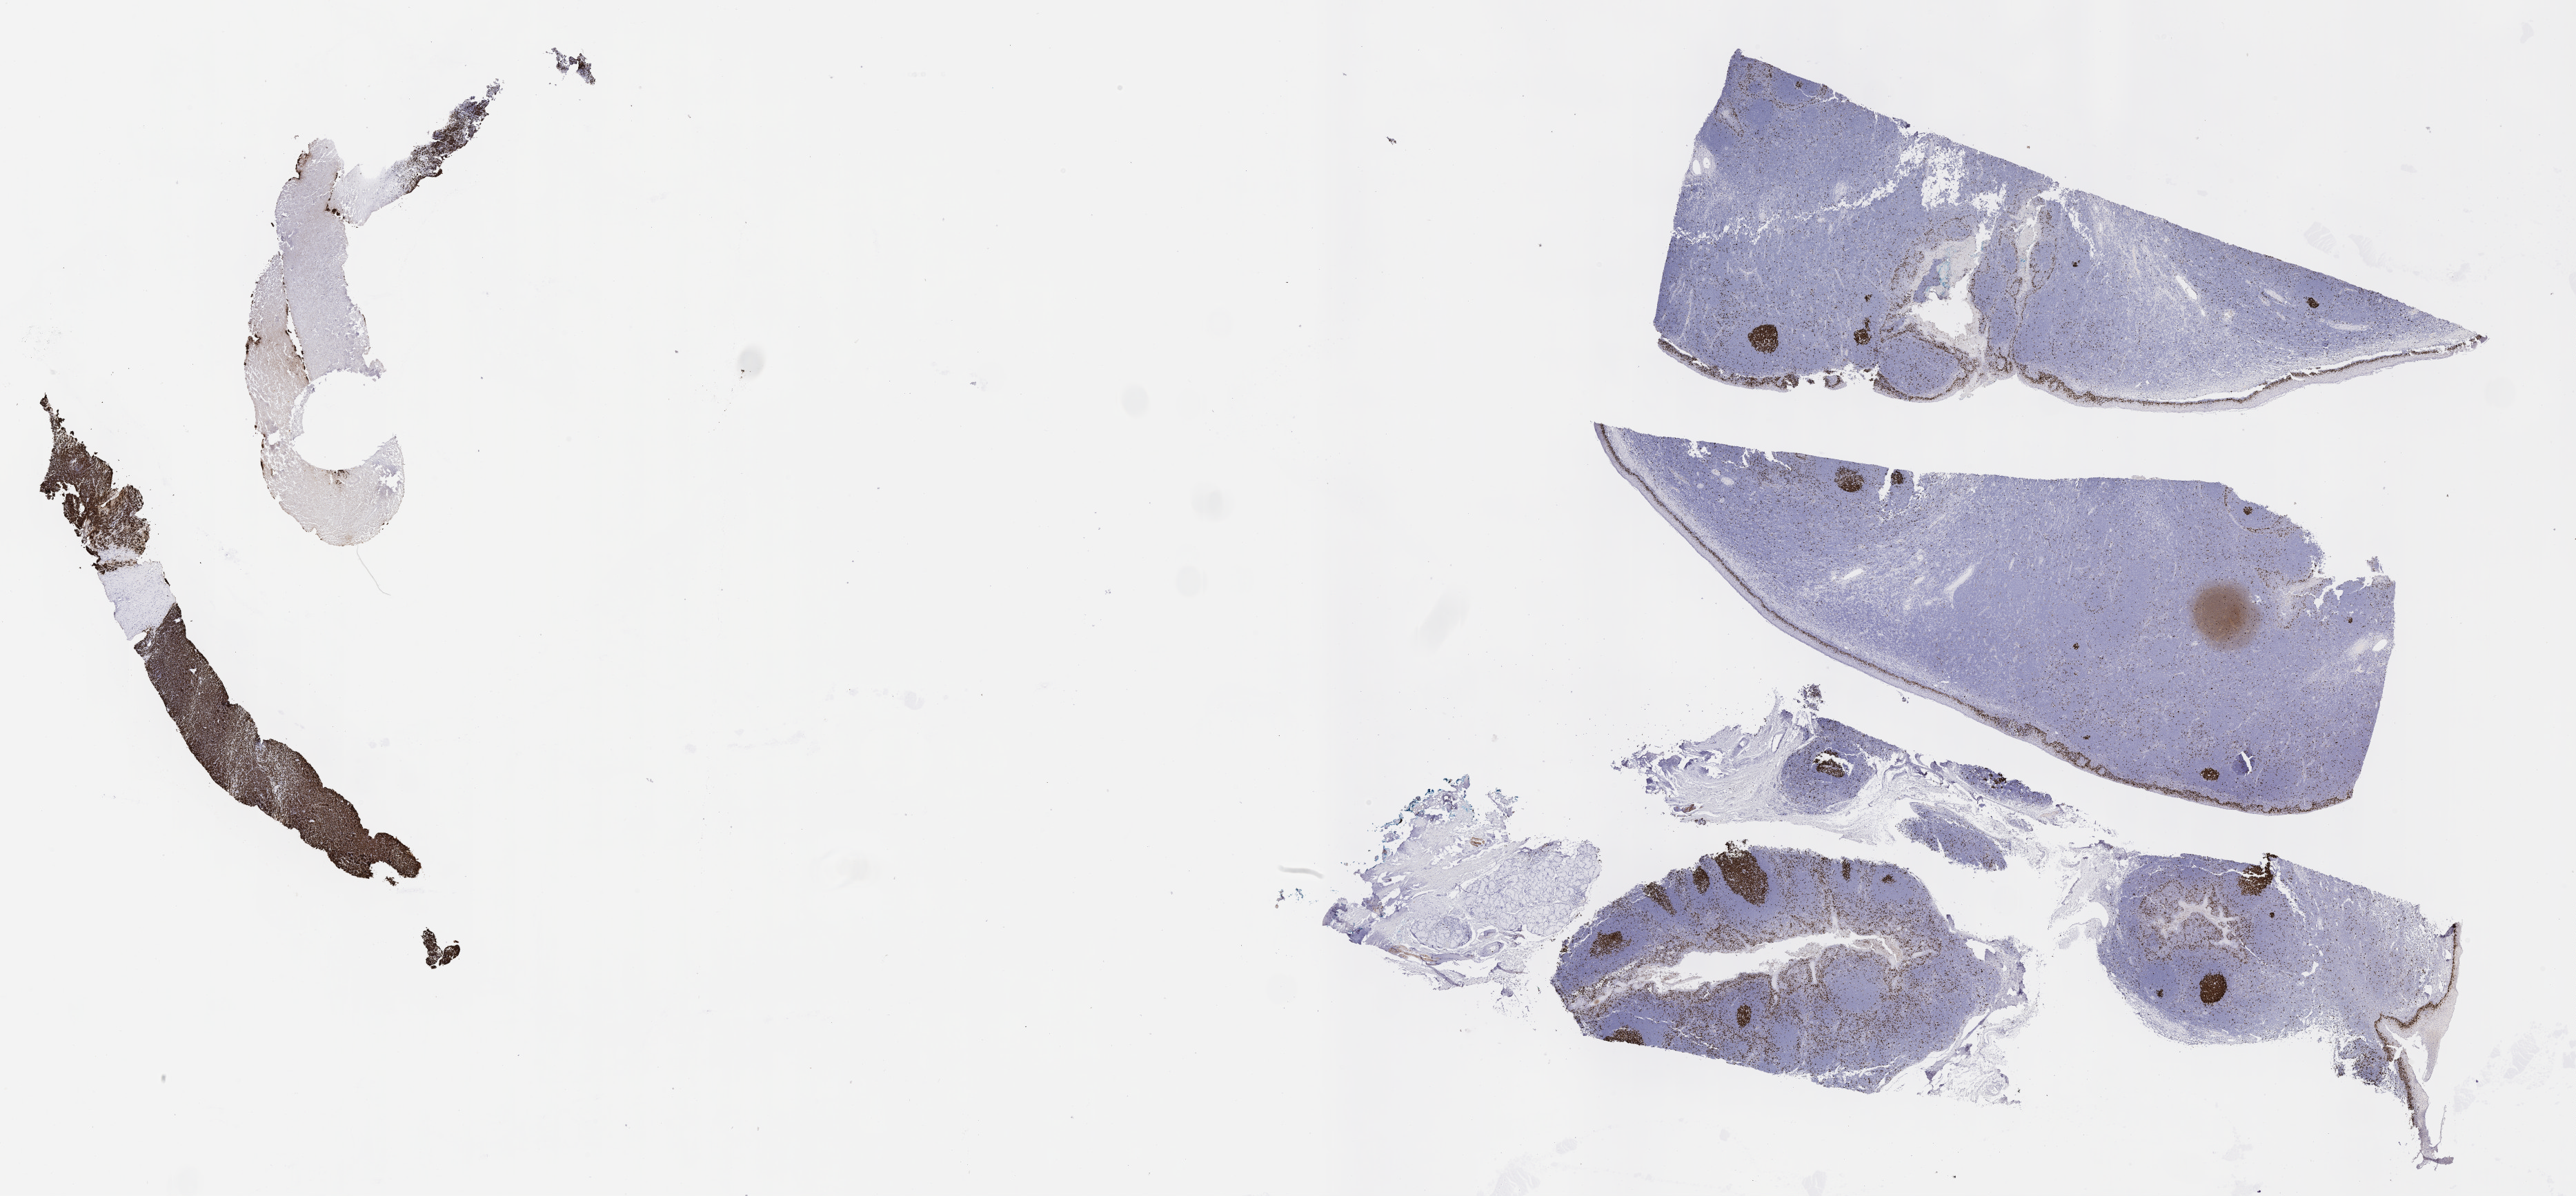
IHC for Ki-67, whole-slide image, a low-resolution overview of the entire scanned area, about 30.2 x 14.0 mm. Specimen: tumor tissue. Male patient, aged 10.
Diagnosis: Burkitt lymphoma, NOS.